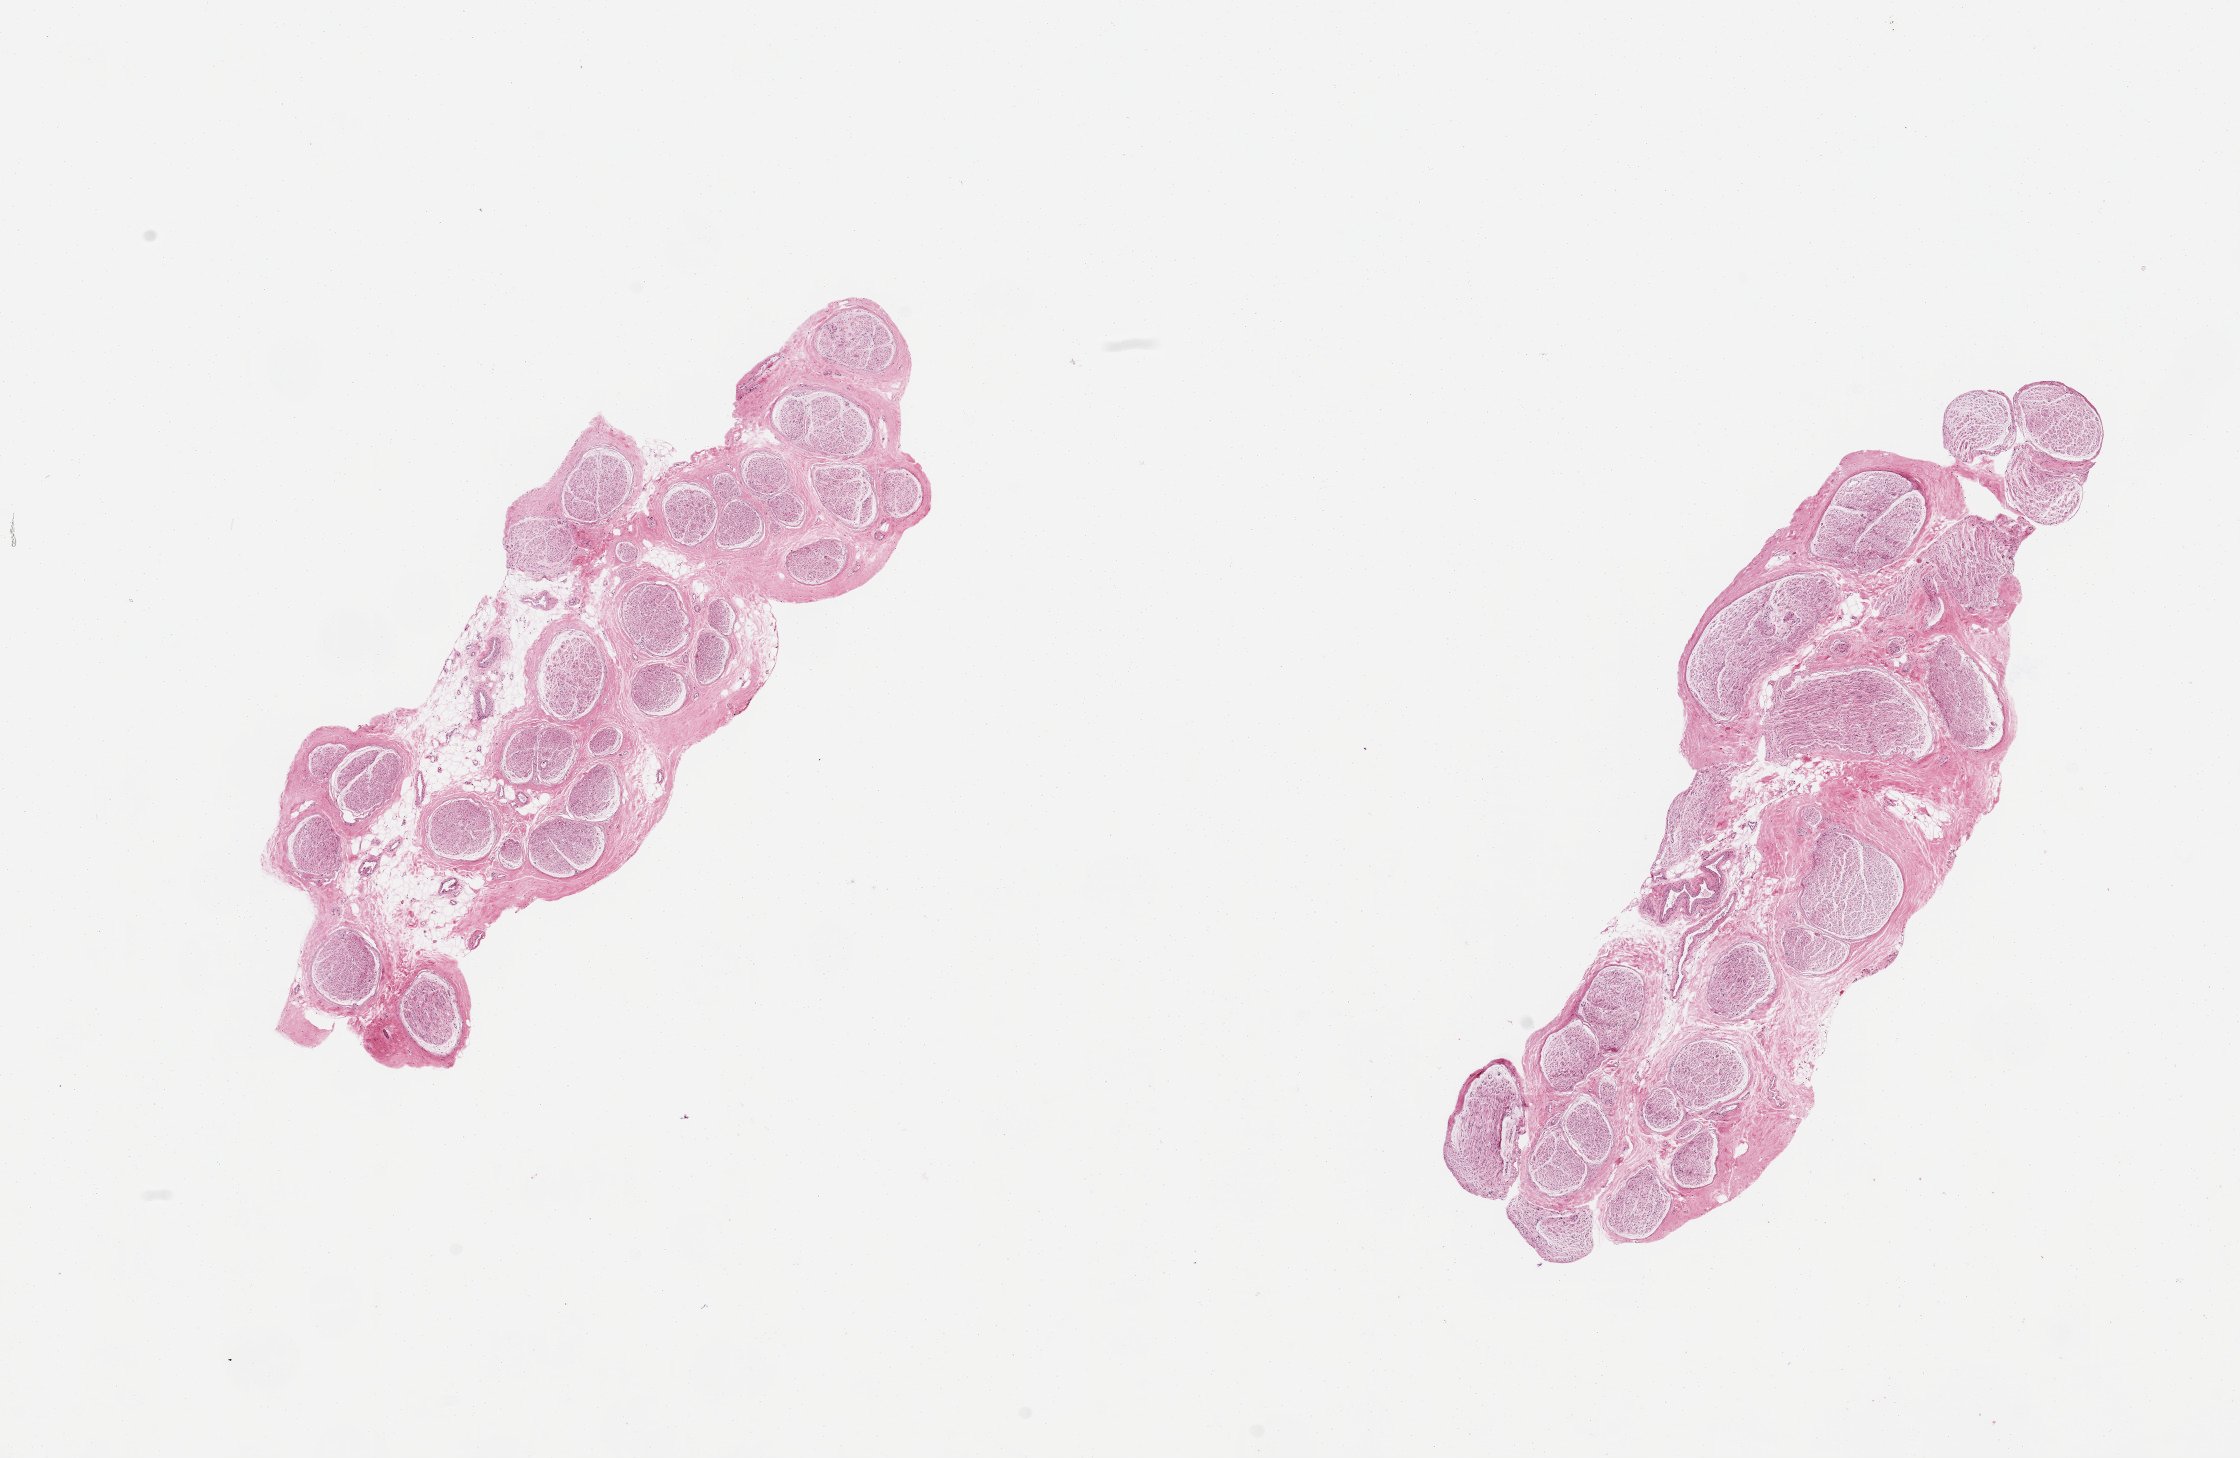
Digitized H&E-stained section, low-resolution overview of the scanned area, about 17.7 x 11.5 mm (acquisition: 20x scan), PAXgene-fixed, paraffin-embedded tissue, section of tibial nerve (target tissue), donor tissue sample. Donor: male.
• review note (as recorded): 2 pieces; well trimmed; up to 20% internal fat; nerve fibers appear swollen